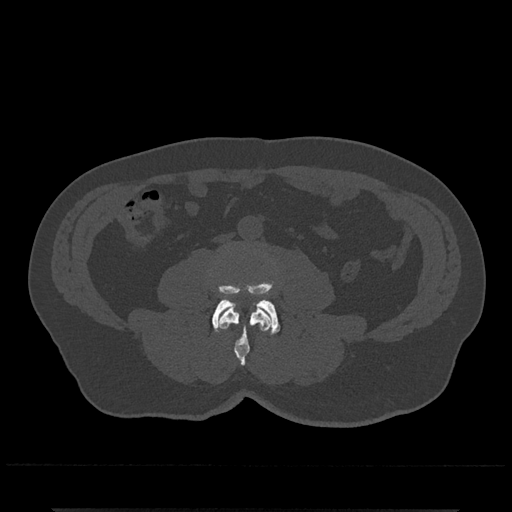
CT including the spine, one axial slice. Position 188 of 797 along the scan axis. Reconstruction kernel Br40s/3. 120 kVp. Bone window (W 1800 / L 400 HU). 0.5 mm slice thickness. 512 × 512 image matrix, field of view 393 × 393 mm. Patient: male, 67 years. From the clinical record (not read from this slice): primary cancer: prostate.
Annotated regions visible in this slice (semi-automatically segmented with operator editing):
- L3 vertebra: bounding box [x1, y1, x2, y2] px = [218, 306, 272, 366]
- L4 vertebra: [212, 283, 280, 334]